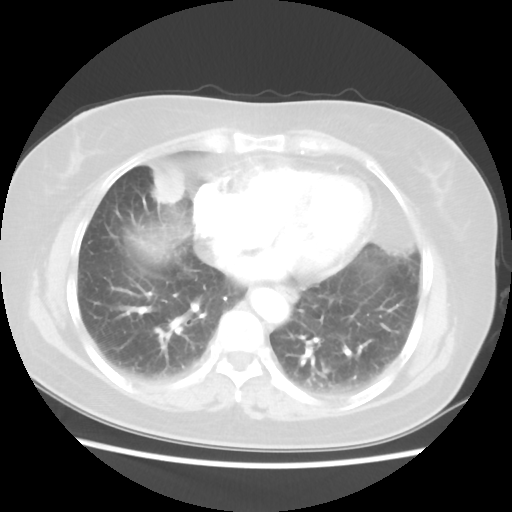
Chest CT, one axial slice; slice 18 of 48 in the series (ordered by position); reconstruction kernel STANDARD; lung window (W 1500 / L -600 HU); 512 × 512 image matrix. Female patient, age 61 years. Case-level facts recorded for this patient, not image findings: clinical TNM (as recorded): T1c N0 M0.
Annotated regions visible in this slice (bounding box drawn by a radiologist):
- lung tumour (recorded histology: adenocarcinoma): bounding box [x1, y1, x2, y2] px = [148, 168, 184, 209]